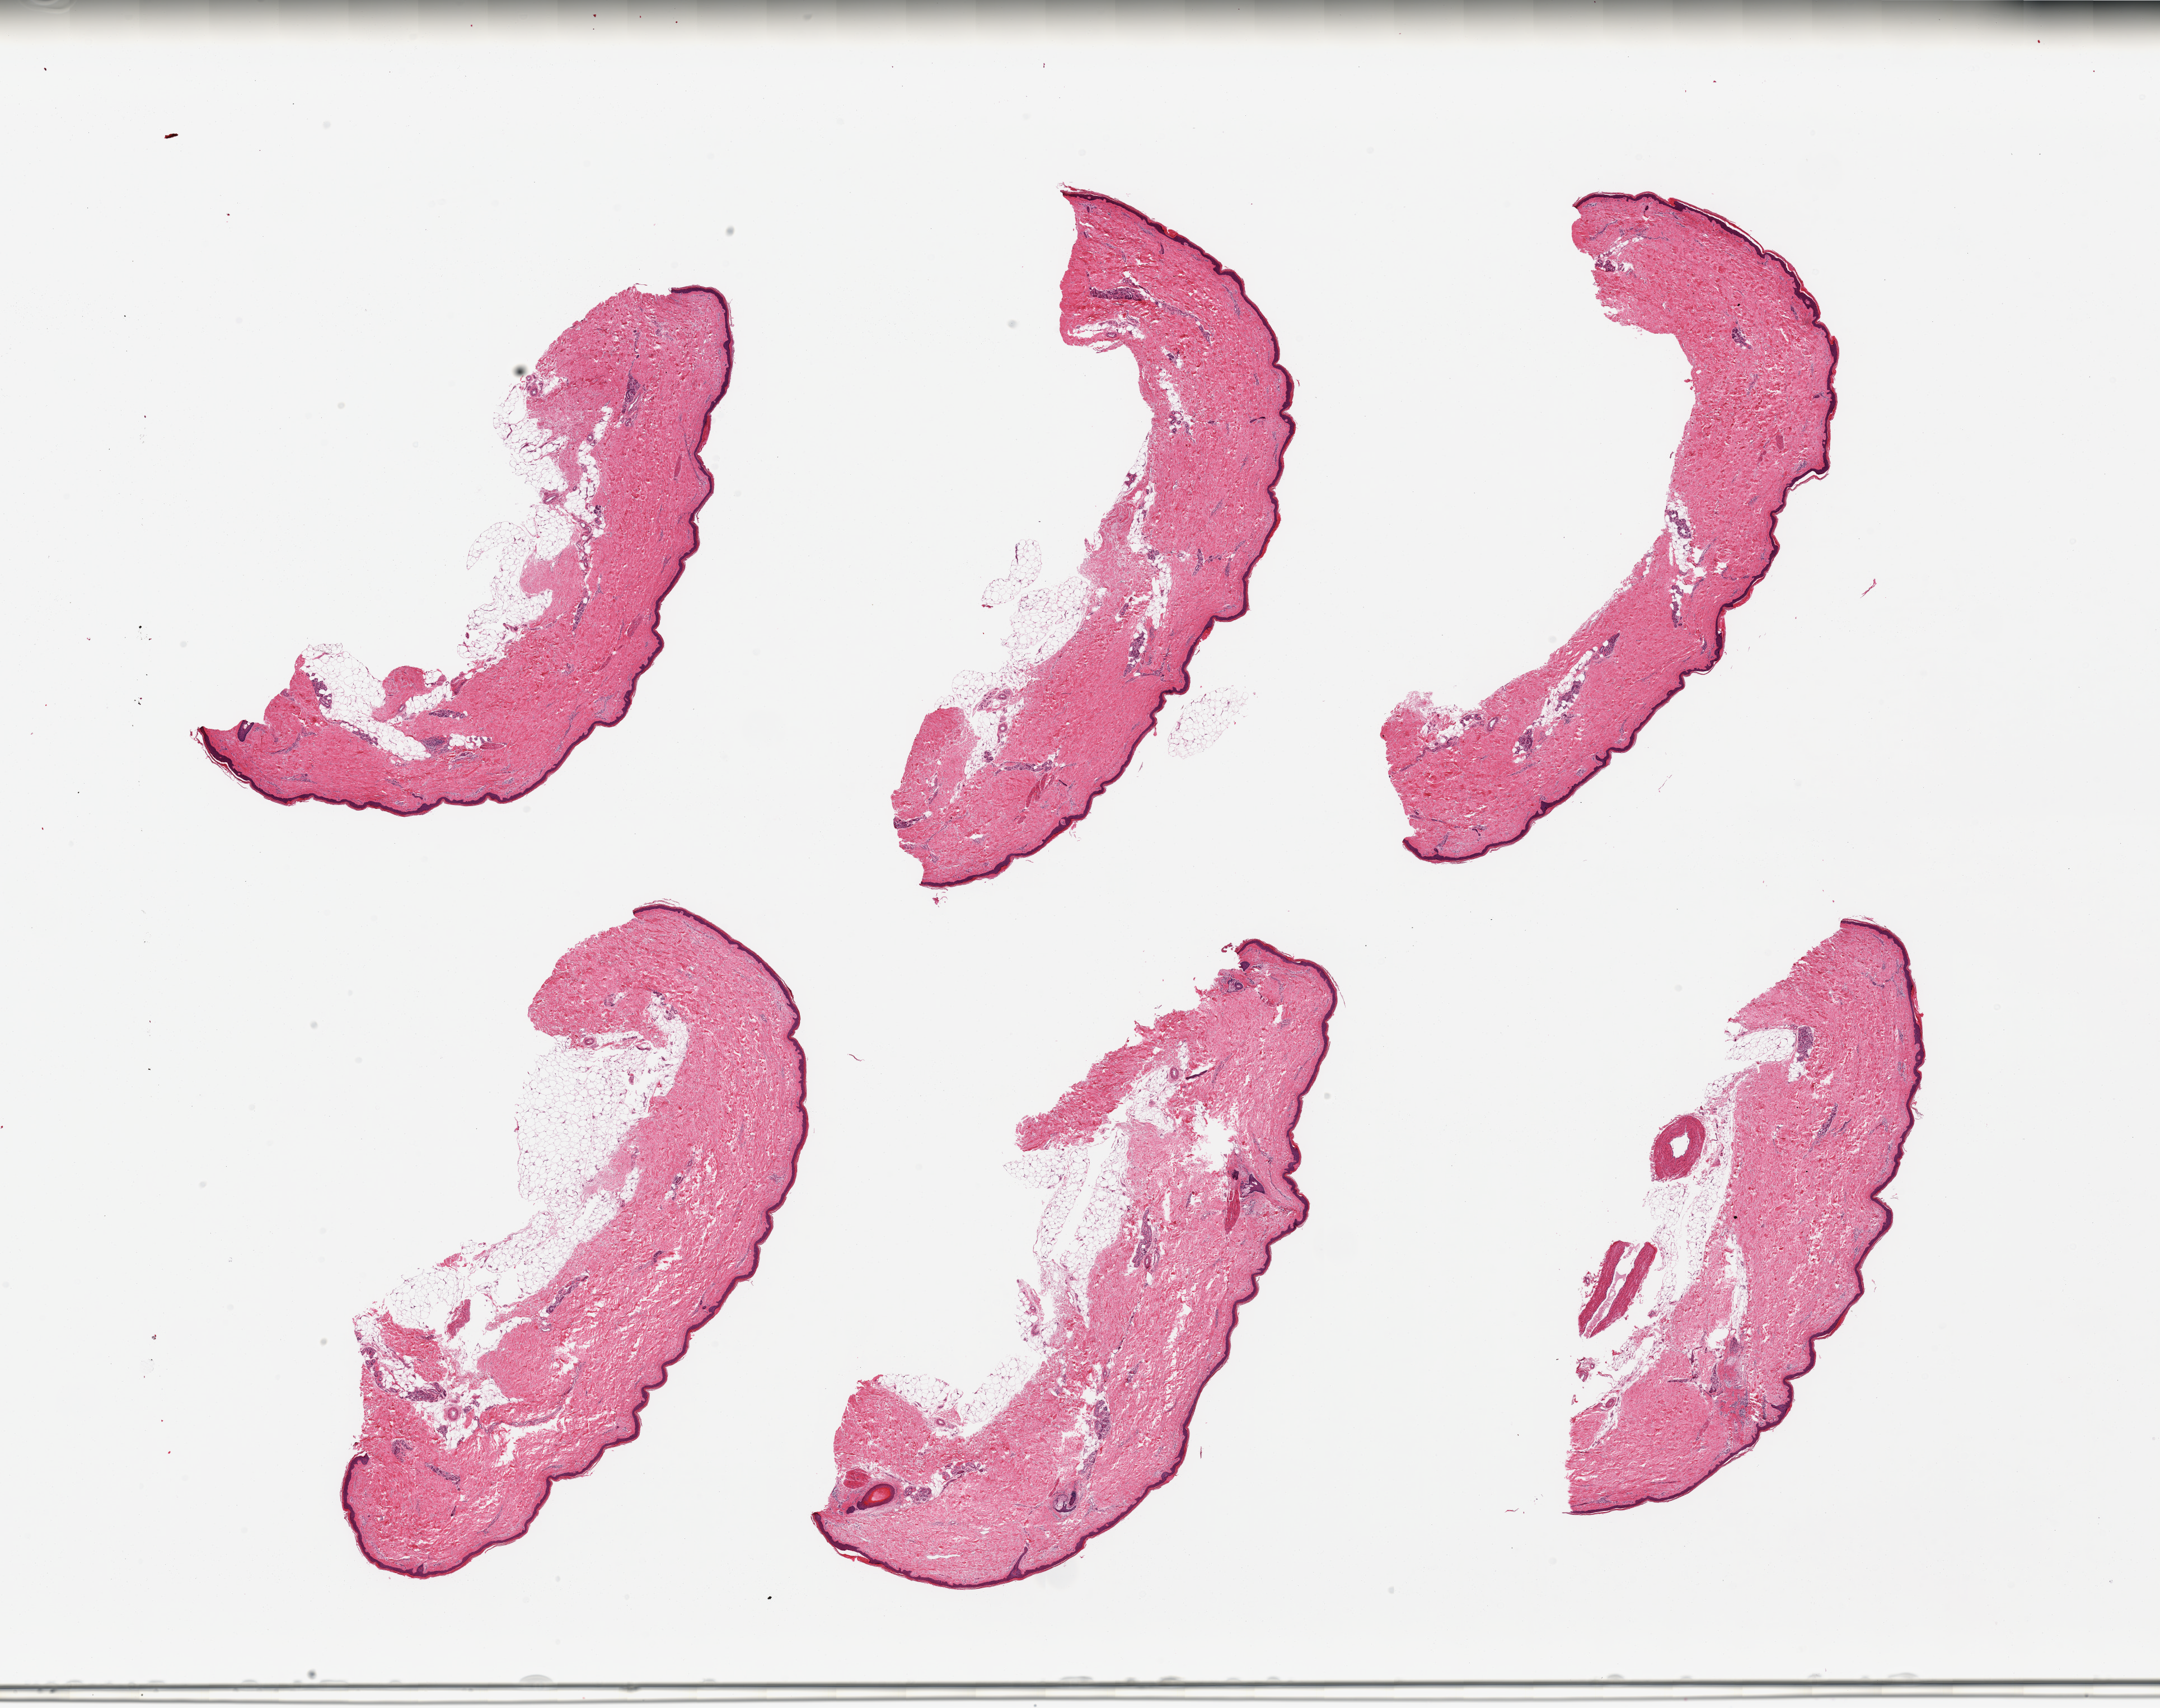
Hematoxylin and eosin (H&E) whole-slide image — whole scanned area (about 30.5 x 24.1 mm, acquisition: 20x scan) shown as a low-resolution overview, PAXgene-fixed, paraffin-embedded tissue, section of skin of lower leg (target tissue), tissue donor sample. Donor: male.
* pathologist's review note for this sample: 6 pieces, moderate dermal fat, focal adherent fat up to ~1.5mm; Squamous epithelium is ~40-50microns